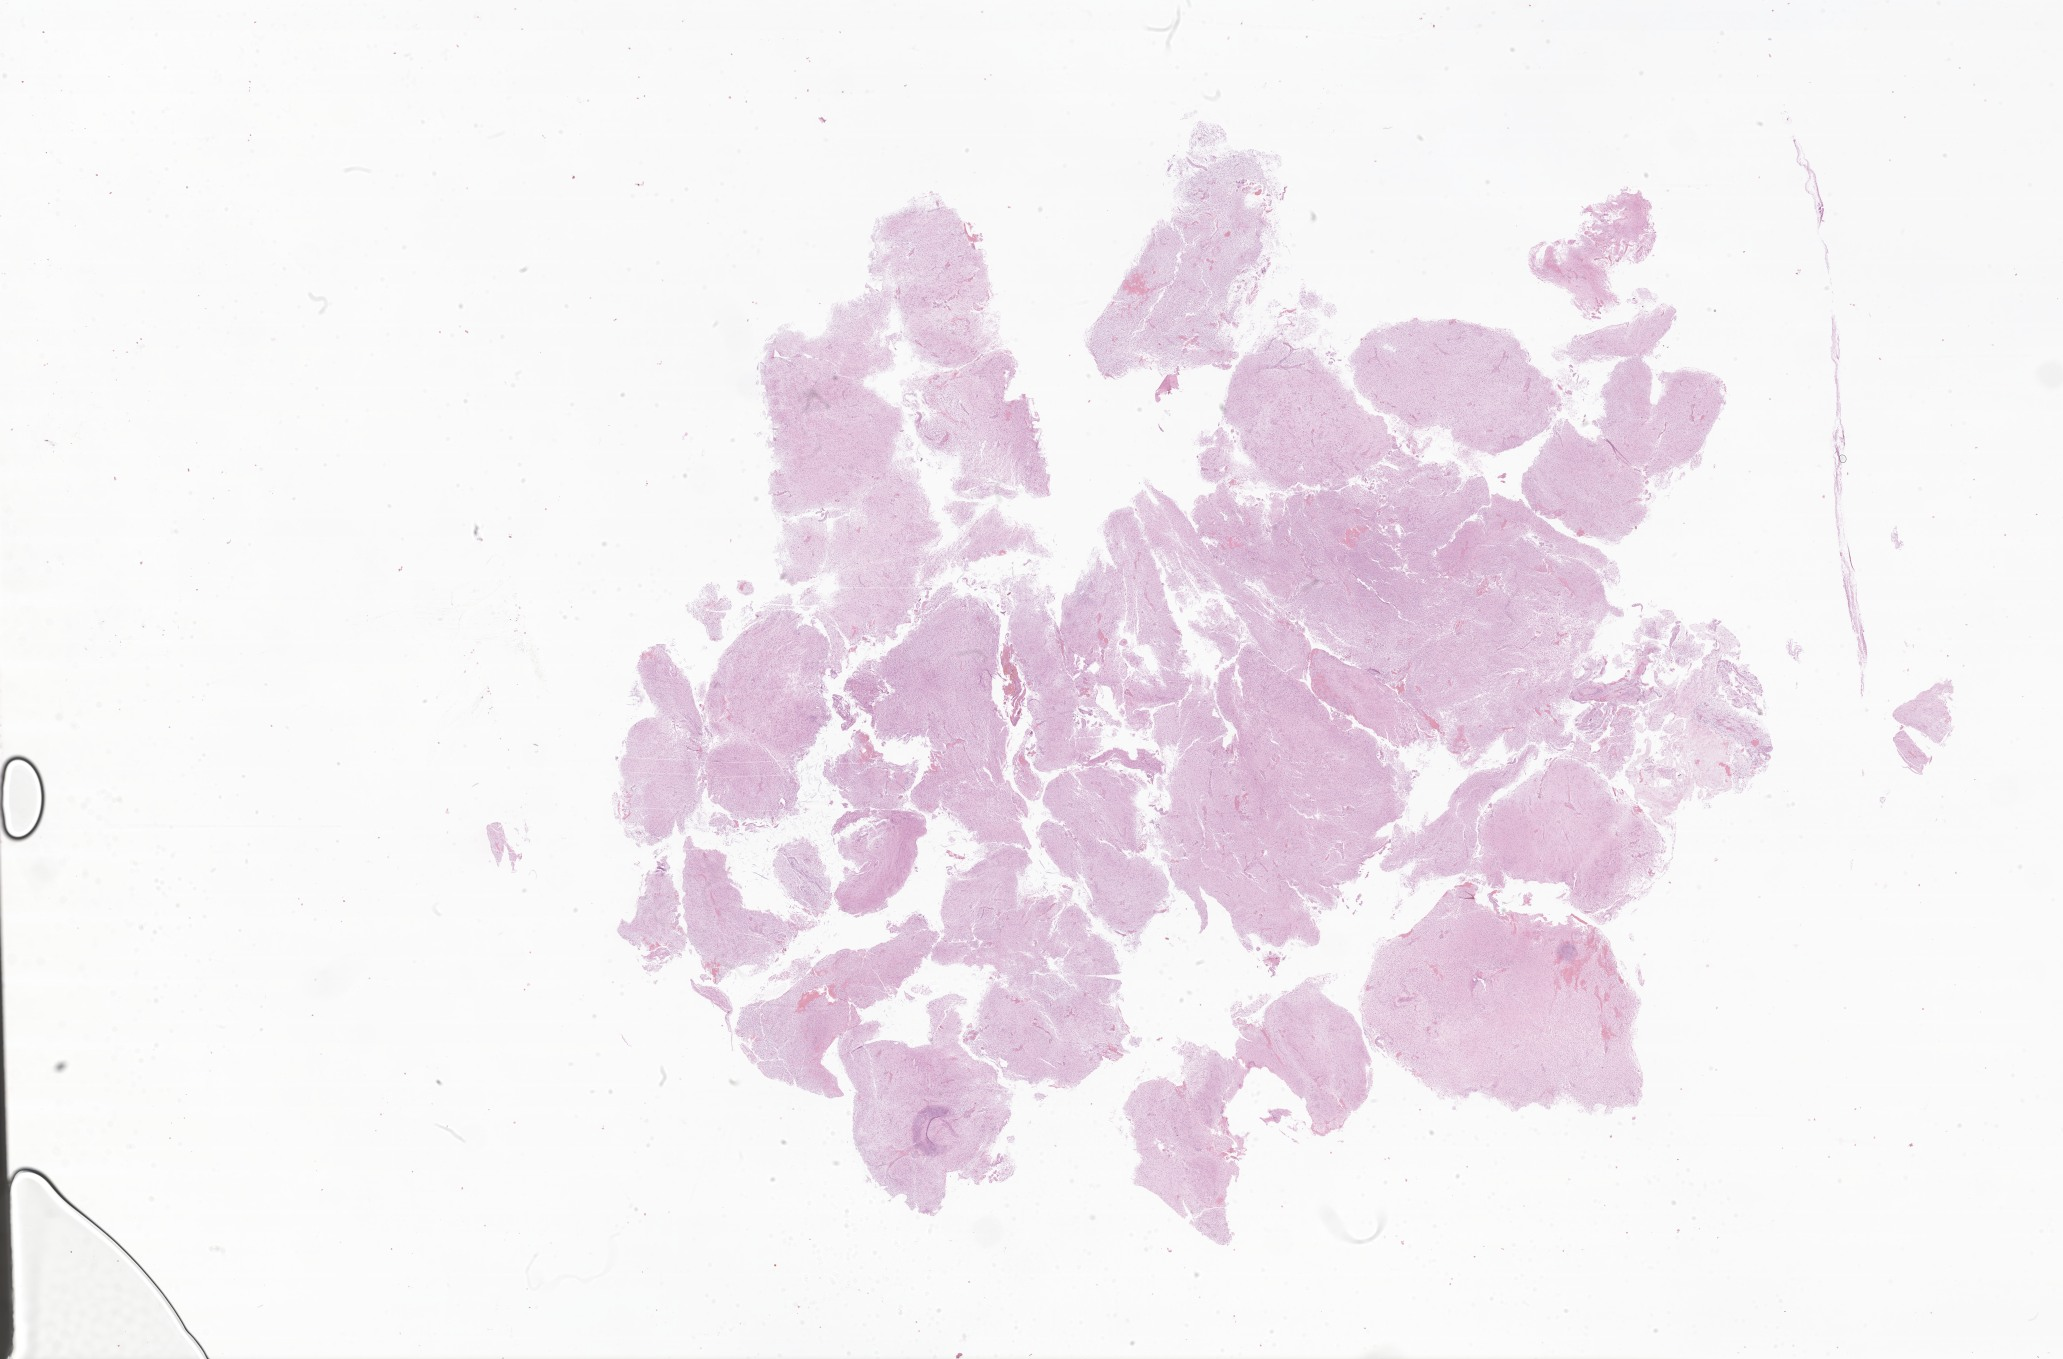
Whole-slide image, haematoxylin and eosin stain of tumor tissue from the central nervous system — low-resolution overview of the scanned area, about 34.8 x 22.9 mm, formalin-fixed, paraffin-embedded (FFPE) tissue. Patient: male, age 34 months (2 years 10 months).
Diagnosis (ICD-O-3 morphology term): Glioma, malignant.